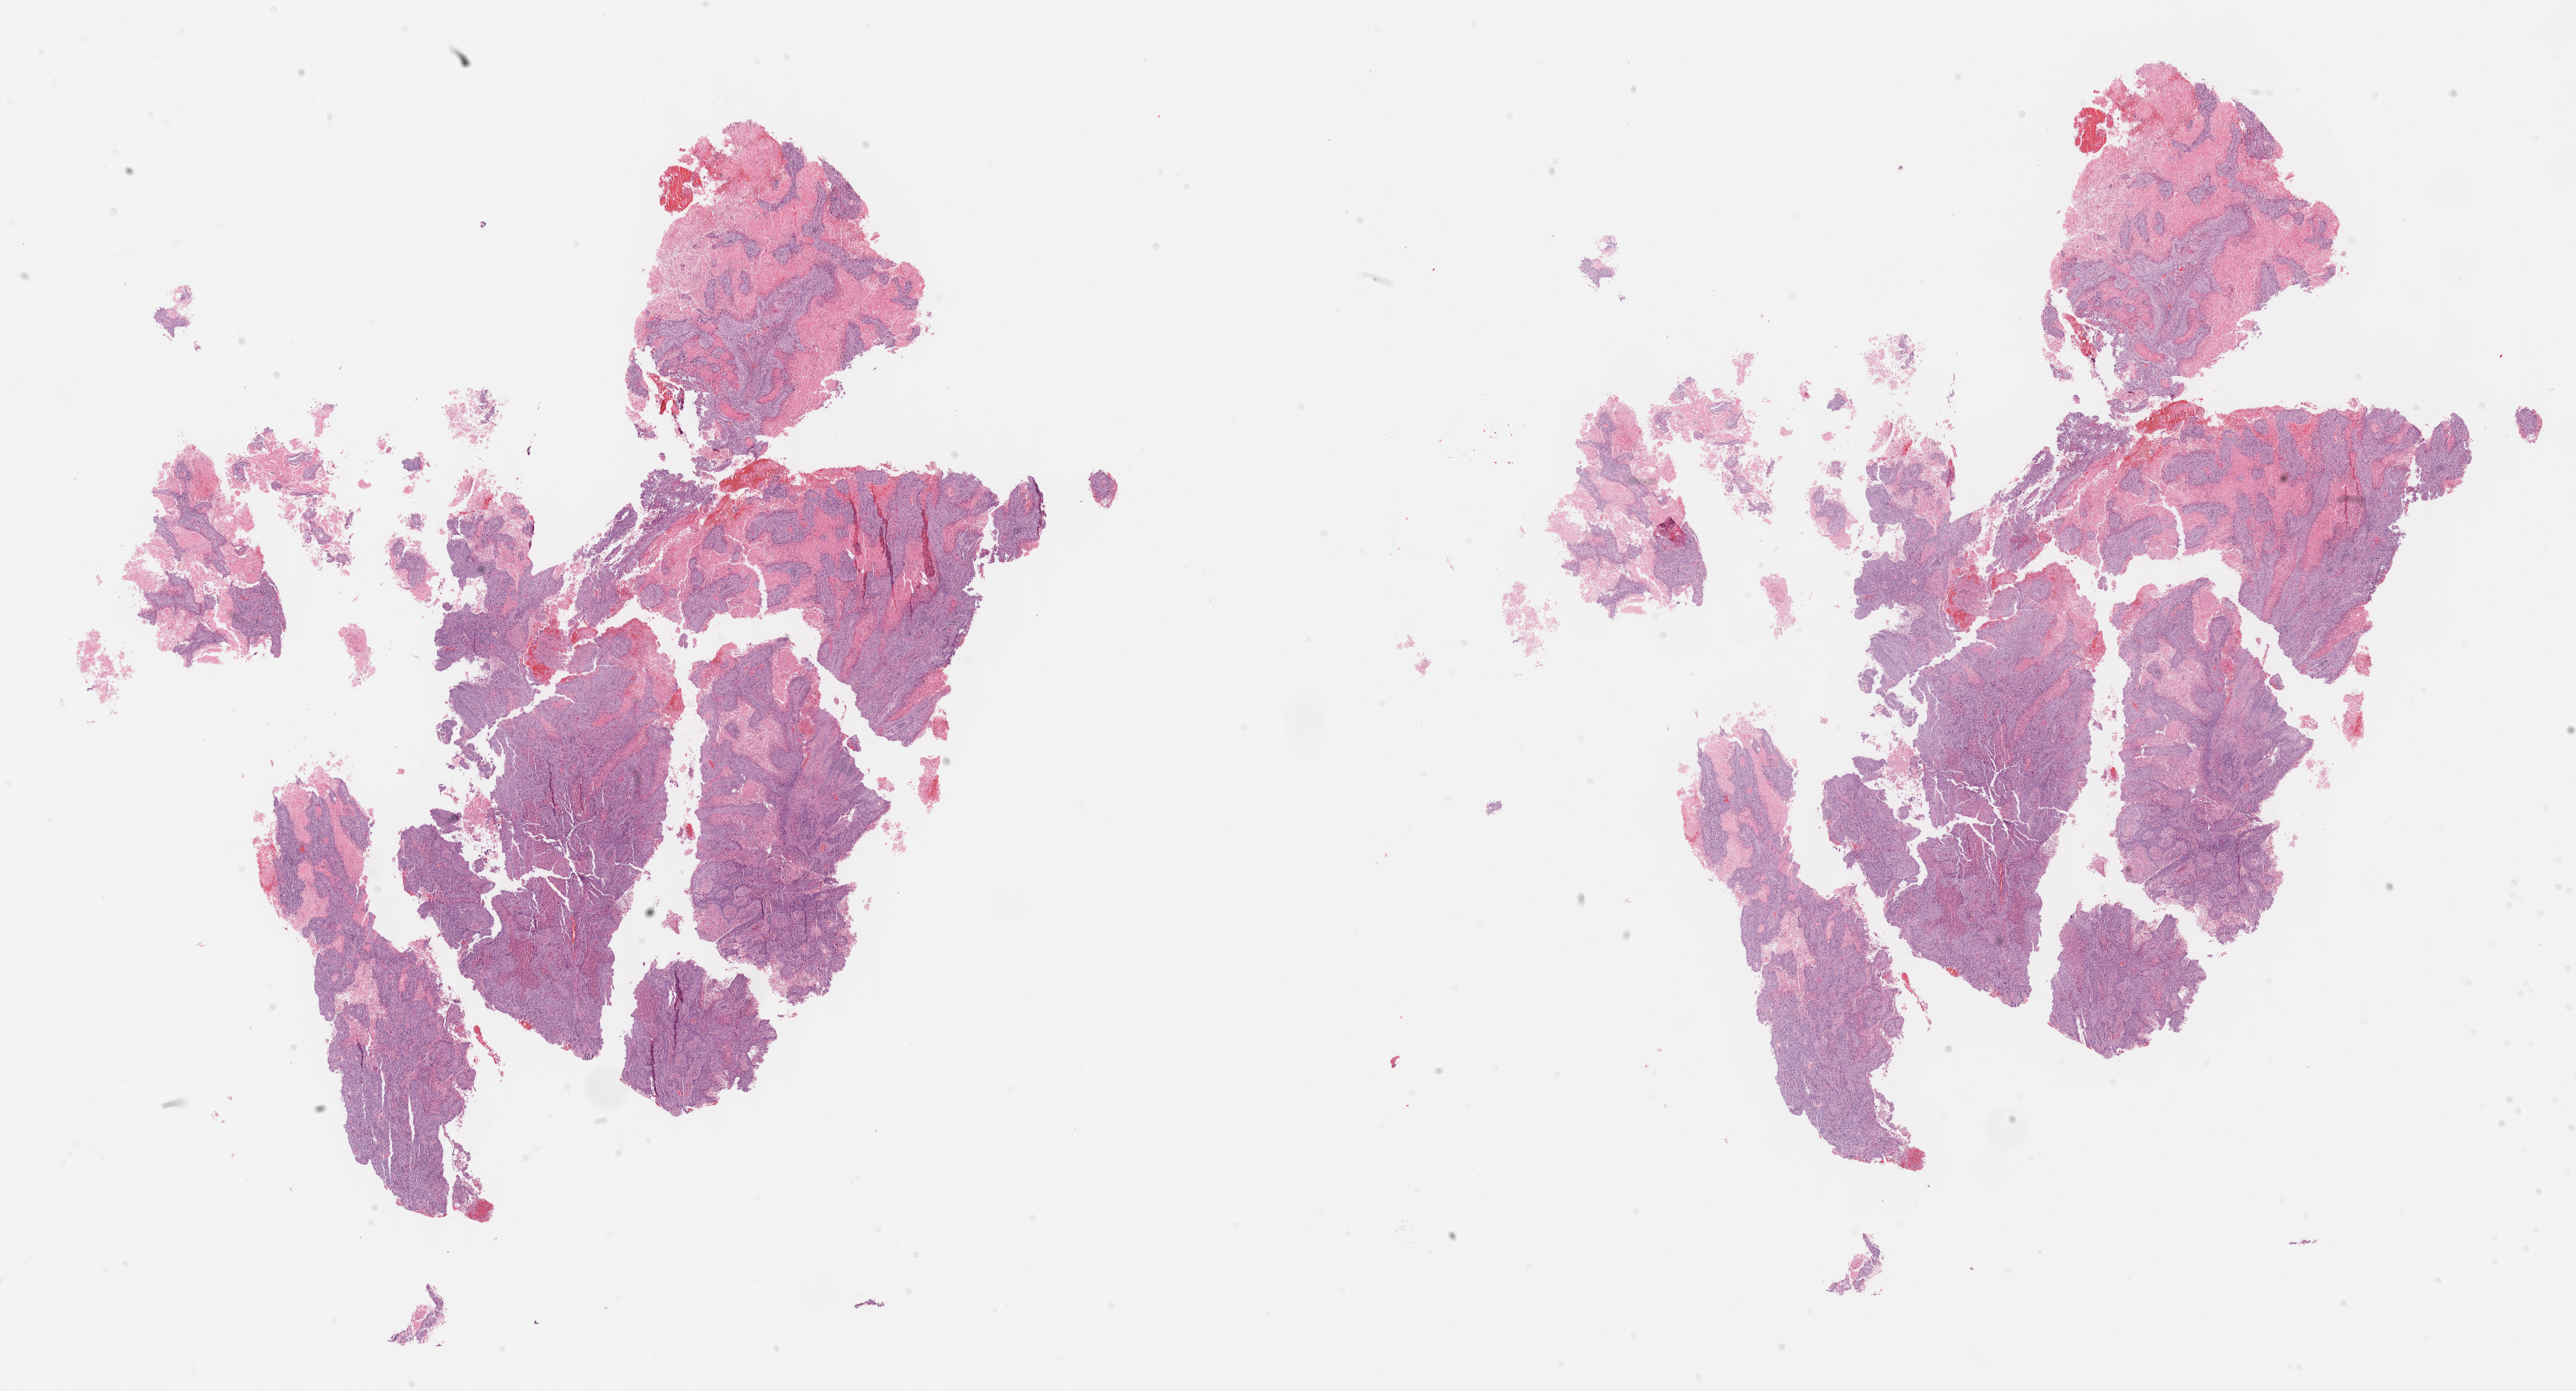
H&E whole-slide image — shown as a low-resolution overview of the whole scanned area (about 31.7 x 17.1 mm), tumor tissue, anatomic site: cervix. Patient: female, 42 years old.
Histologic diagnosis: Squamous cell carcinoma, keratinizing, NOS.